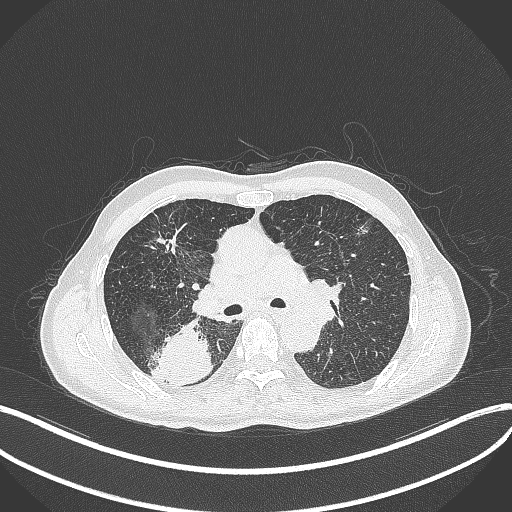
Chest CT, one axial slice. Position 280 of 428 along the scan axis. Reconstruction kernel B70f. Lung window (W 1500 / L -600 HU). 1 mm slice thickness. 512 × 512 image matrix. Male patient, age 79 years. Case-level facts recorded for this patient, not image findings: clinical TNM (as recorded): T3 N0 M0.
Outlined on this slice (rectangle marked by the reading radiologist):
- lung tumour (recorded histology: adenocarcinoma): bounding box (x1, y1, x2, y2) in pixels: (149, 319, 215, 385)